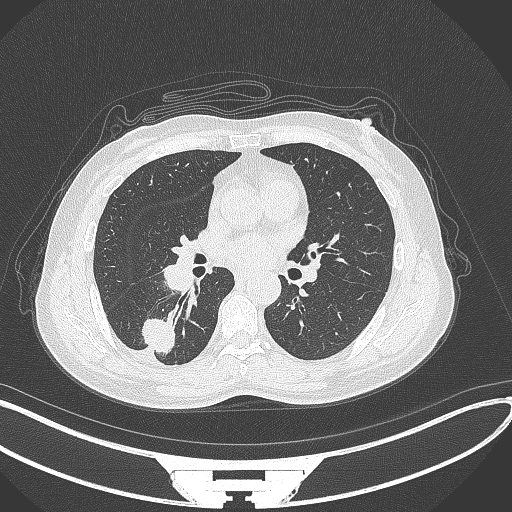
Chest CT, one axial slice. Slice 156 of 352 in the series (ordered by position). Reconstruction kernel B70f. 120 kVp. Lung window (W 1500 / L -600 HU). 1 mm slice thickness. 512 × 512 image matrix. Patient: female, 55 years. From the clinical record (not read from this slice): clinical TNM (as recorded): T1c N1 M0.
Annotated regions visible in this slice (bounding box drawn by a radiologist):
- lung tumour (recorded histology: adenocarcinoma): bounding box [x1, y1, x2, y2] px = [138, 314, 180, 356]